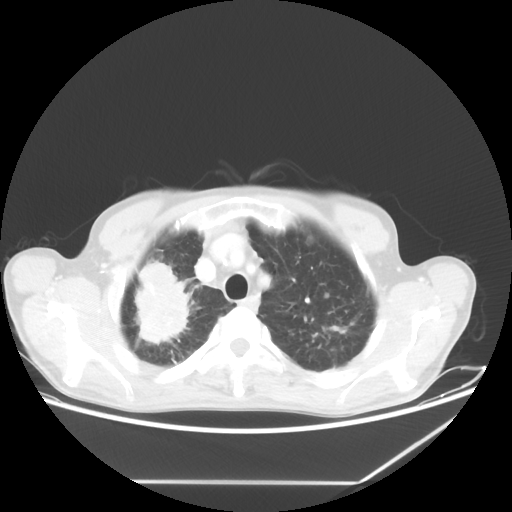
Chest CT, one axial slice. Slice 53 of 65 in the series (ordered by position). 80 kVp. Lung window (W 1500 / L -600 HU). 512 × 512 image matrix. Male patient, age 68 years. From the clinical record (not read from this slice): clinical TNM (as recorded): T3 N3 M0.
Annotated regions visible in this slice (bounding box drawn by a radiologist):
- lung tumour (recorded histology: adenocarcinoma): box from (x=114, y=246) to (x=198, y=359) px